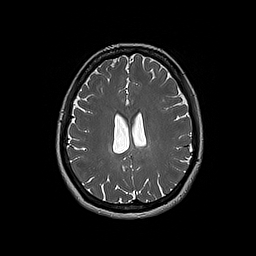
Brain MRI from a brain-tumour surgery series, one axial slice. Position 74 of 192 along the scan axis. 1 mm slice thickness. 256 × 256 image matrix, field of view 250 × 250 mm. From the clinical record (not read from this slice): histopathology: Oligodendroglioma; WHO grade: 2.
Structures marked on this image (manually delineated by an expert):
- tumour: bounding box <109,147,112,153> (left, top, right, bottom; pixels)